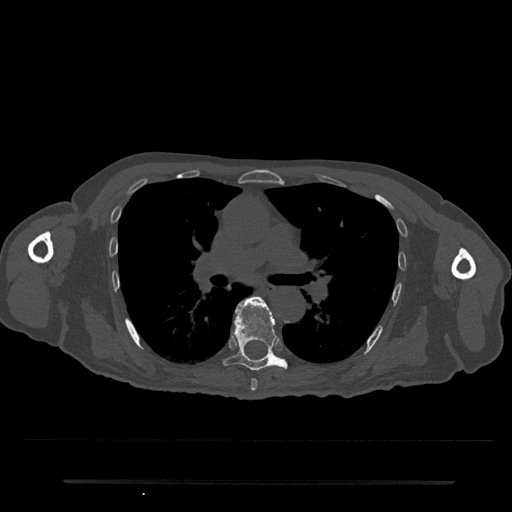
CT including the spine, one axial slice. Position 488 of 797 along the scan axis. Reconstruction kernel Br40s/3. 120 kVp. Bone window (W 1800 / L 400 HU). 0.5 mm slice thickness. 512 × 512 image matrix. Patient: male, 74 years. From the clinical record (not read from this slice): primary cancer: prostate.
Outlined on this slice (semi-automatically segmented with operator editing):
- T6 vertebra: bounding box [x1, y1, x2, y2] px = [250, 379, 258, 391]
- T7 vertebra: [221, 297, 288, 371]